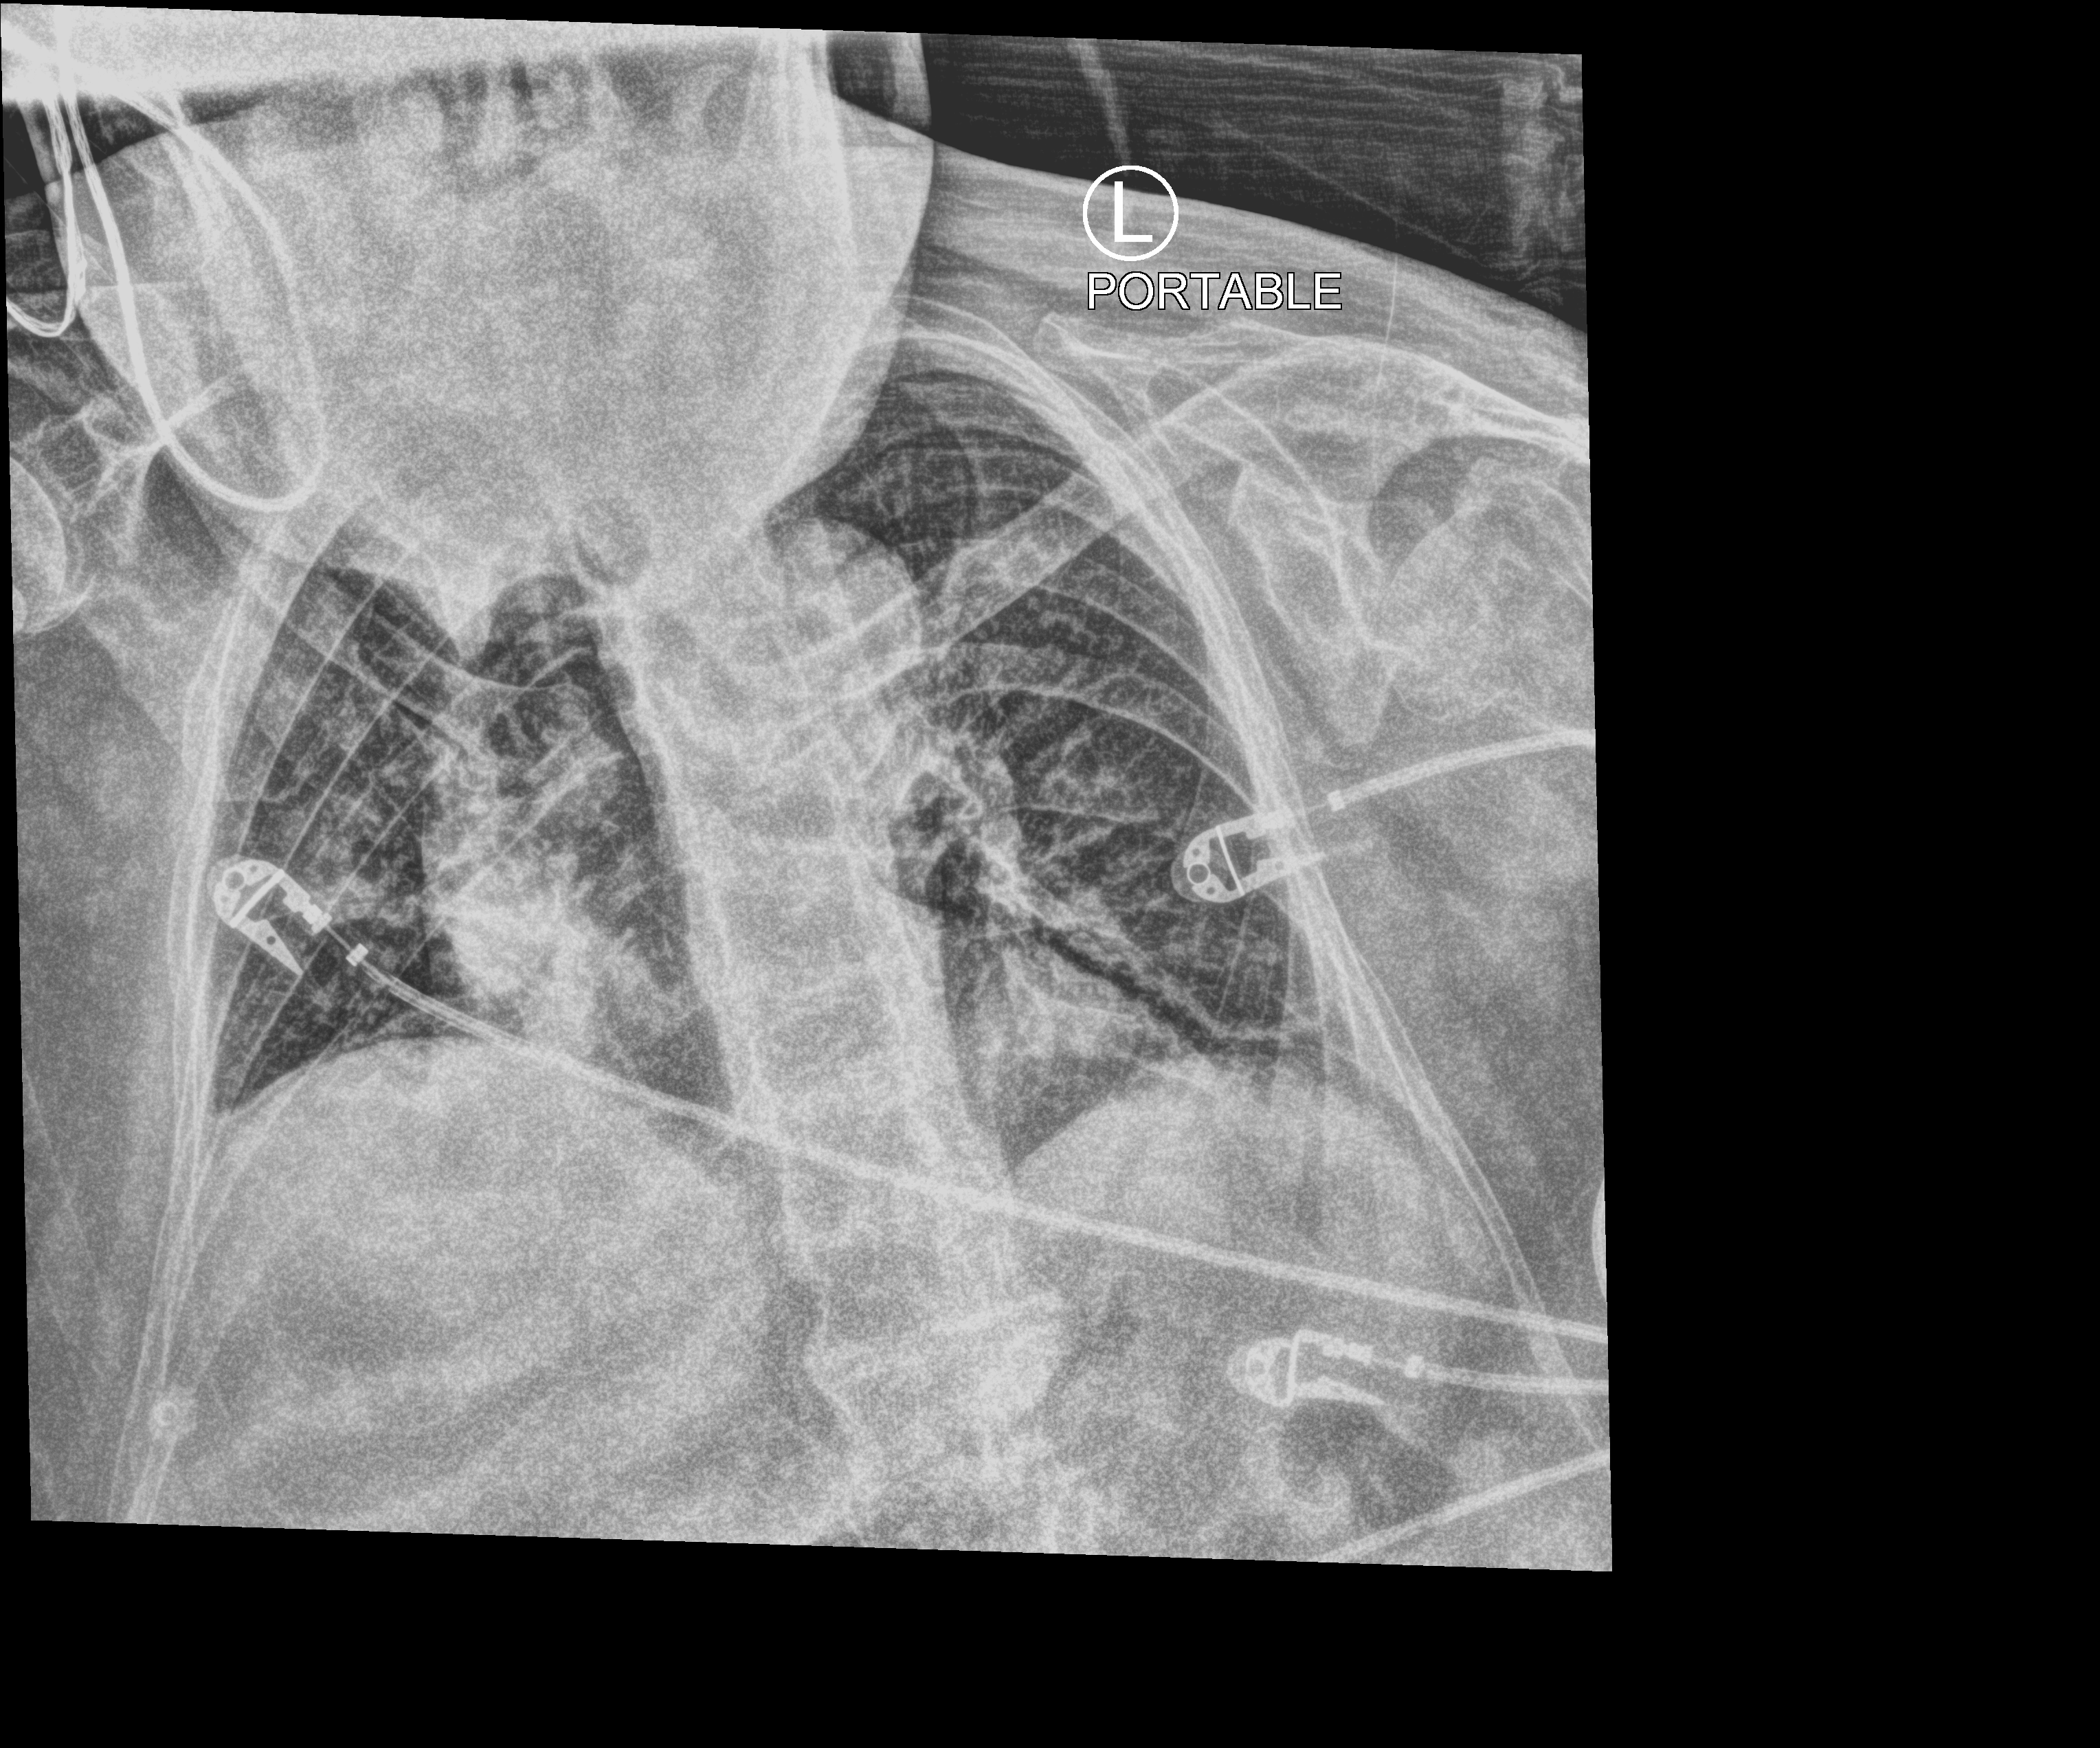
Bedside chest radiograph (computed radiography). Female patient hospitalised with COVID-19, age 75–90 years.
Hospital-stay facts (about this admission, not read from this image; timing relative to this image not recorded):
- admitted to intensive care during this hospital stay: yes
- other chronic lung disease (admission record): no